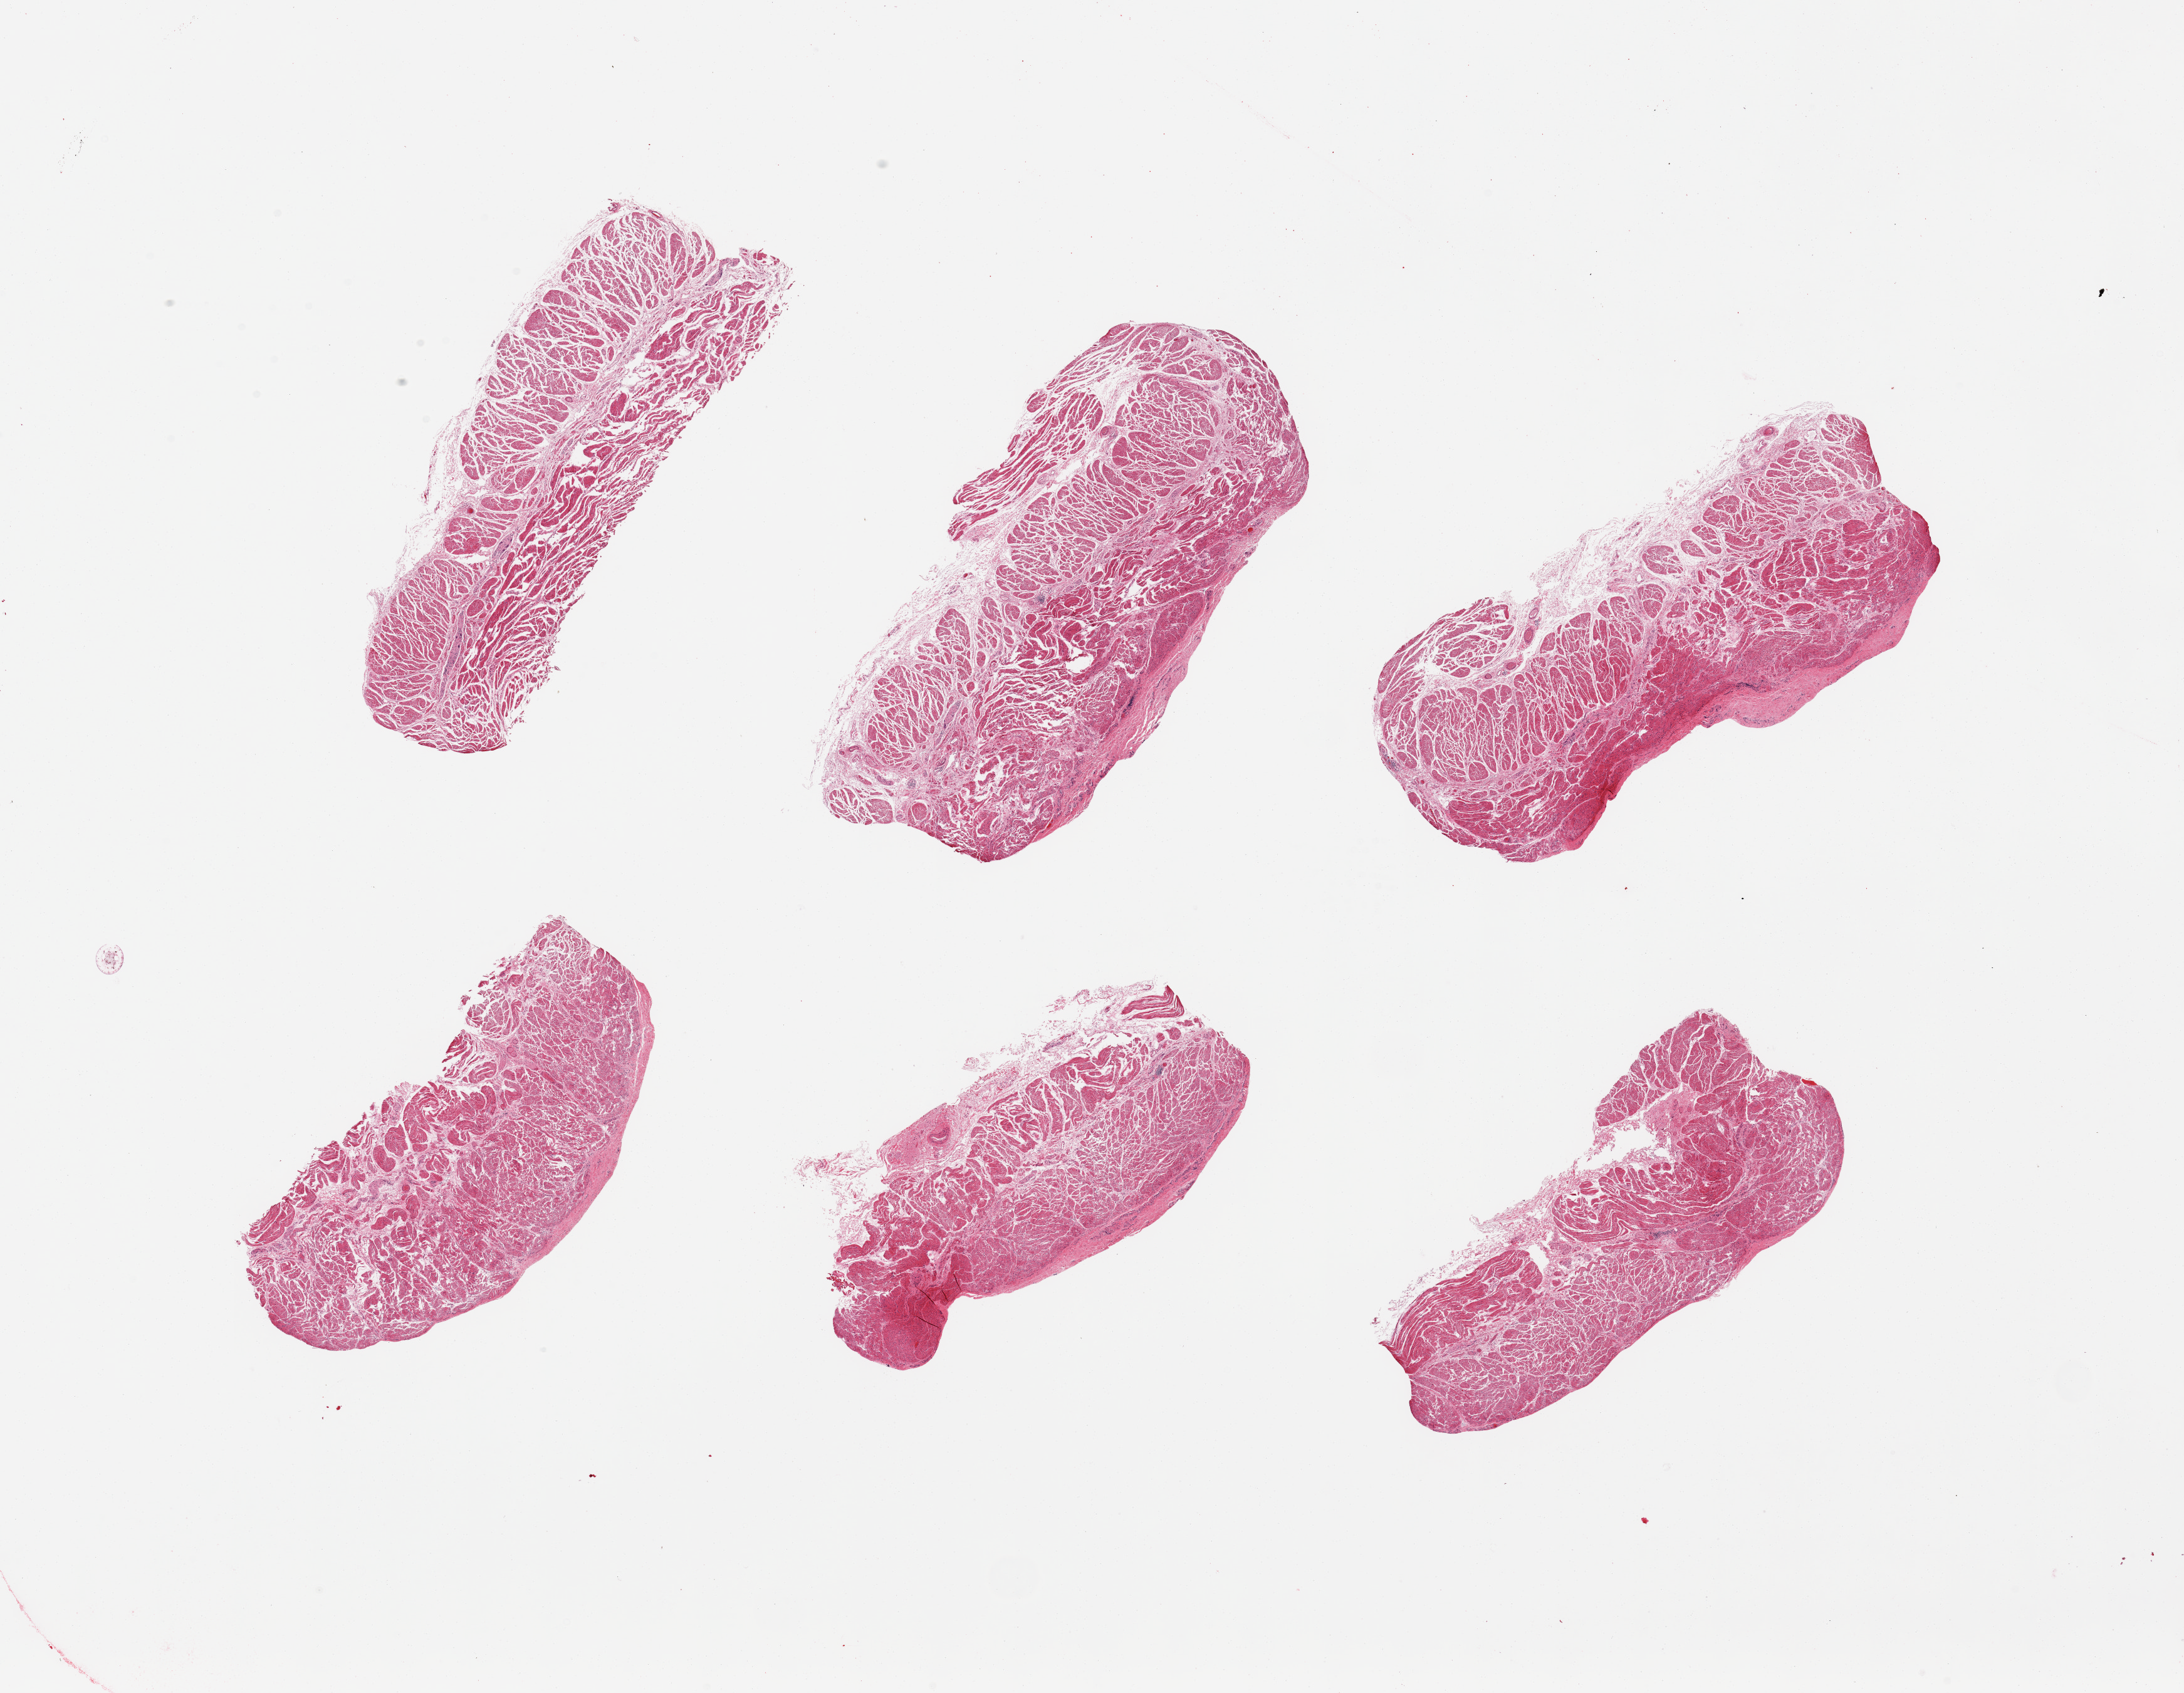
Haematoxylin and eosin whole-slide image — low-resolution overview of the scanned area, about 27.6 x 21.4 mm. PAXgene-fixed, paraffin-embedded tissue. Target tissue: gastroesophageal junction. Tissue donor sample. Donor: male.
Review note (as recorded): 6 pieces; well dissected.